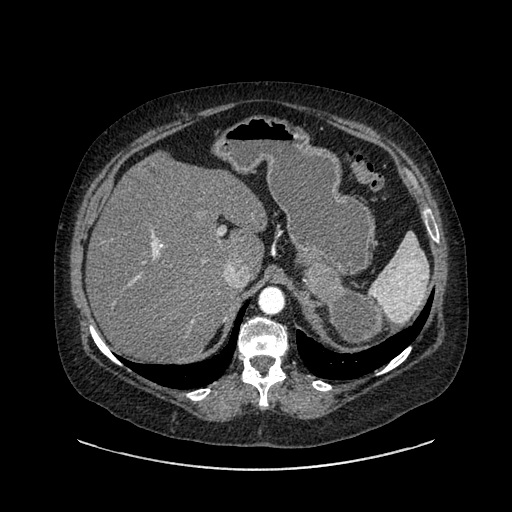
Contrast-enhanced abdominal CT, one axial slice; position 625 of 769 along the scan axis; intravenous contrast given; soft-tissue window (W 400 / L 40 HU); 0.62 mm slice thickness; 512 × 512 image matrix, field of view 460 × 460 mm. Female patient, age 61 years. From the clinical record (not read from this slice): diagnosis: adrenocortical carcinoma; tumour side: left adrenal; tumour size at pathology: 13 cm.
Structures marked on this image (semi-automatically segmented with operator editing):
- mass: bounding box [x1, y1, x2, y2] px = [301, 240, 512, 346]